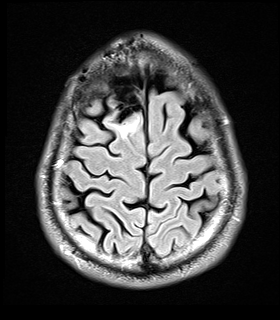
Brain MRI from a brain-tumour surgery series, one axial slice. Slice 6 of 32 in the series (ordered by position). T2 FLAIR. 280 × 320 image matrix, field of view 184 × 210 mm. From the clinical record (not read from this slice): histopathology: Glial fibroma.
Structures marked on this image (manually delineated by an expert):
- tumour: bounding box [x1, y1, x2, y2] px = [104, 115, 139, 137]